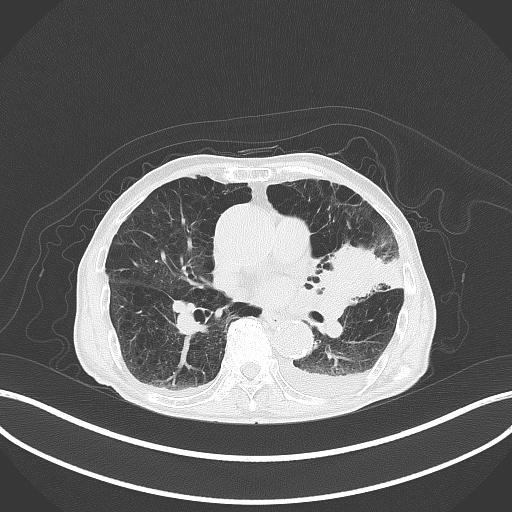
Chest CT, one axial slice. Slice 186 of 227 in the series (ordered by position). 120 kVp. Lung window (W 1500 / L -600 HU). 512 × 512 image matrix. Patient: male, 90 years or older. Case-level facts recorded for this patient, not image findings: clinical TNM (as recorded): T2b N1 M0.
Outlined on this slice (bounding box drawn by a radiologist):
- lung tumour (recorded histology: squamous cell carcinoma): box from (x=314, y=240) to (x=402, y=301) px